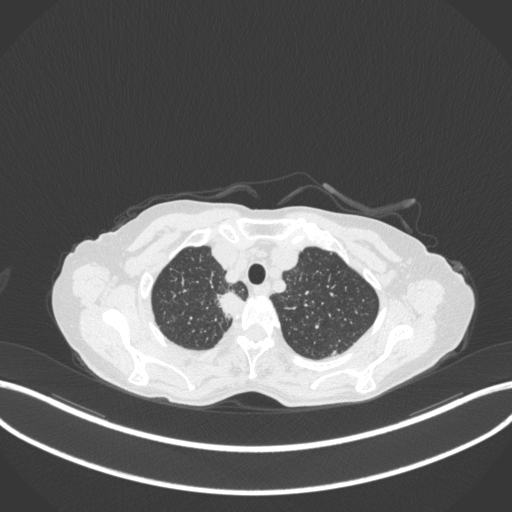
Chest CT, one axial slice; slice 318 of 363 in the series (ordered by position); reconstruction kernel B31f; lung window (W 1500 / L -600 HU); 512 × 512 image matrix. Female patient, age 75 years. From the clinical record (not read from this slice): clinical TNM (as recorded): T1c N1 M1.
Outlined on this slice (bounding box drawn by a radiologist):
- lung tumour (recorded histology: adenocarcinoma): box from (x=214, y=290) to (x=248, y=325) px